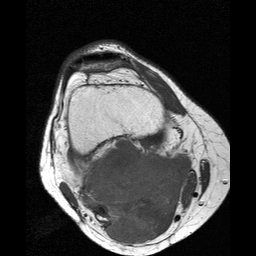
MRI of an extremity soft-tissue mass, one axial slice; slice 14 of 25 in the series (ordered by position); 256 × 256 image matrix, field of view 160 × 160 mm. Female patient. From the clinical record (not read from this slice): histological type: liposarcoma; site of the primary tumour: right thigh.
Annotated regions visible in this slice (manually delineated by an expert):
- gross tumour volume (mass): box from (x=78, y=139) to (x=192, y=243) px